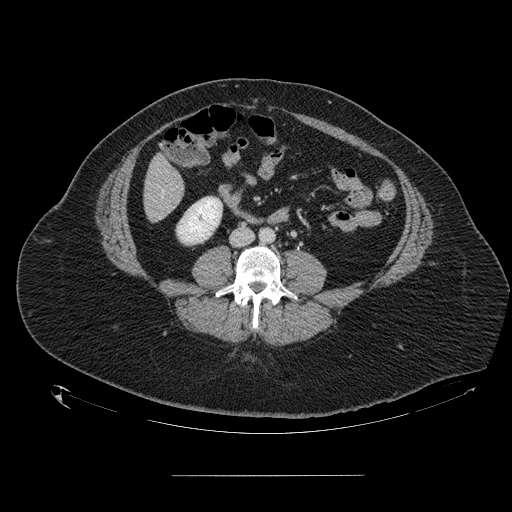
Contrast-enhanced abdominal CT, one axial slice. Position 22 of 164 along the scan axis. 120 kVp. Intravenous contrast given. Soft-tissue window (W 400 / L 40 HU). 2.5 mm slice thickness. 512 × 512 image matrix, field of view 495 × 495 mm. Female patient, age 52 years. Case-level facts recorded for this patient, not image findings: diagnosis: colorectal cancer liver metastases, imaged before liver resection; multiple liver metastases: yes; largest metastasis: 3.5 cm; disease in both lobes: no.
Structures marked on this image (manually delineated by an expert):
- liver: box from (x=145, y=156) to (x=184, y=221) px